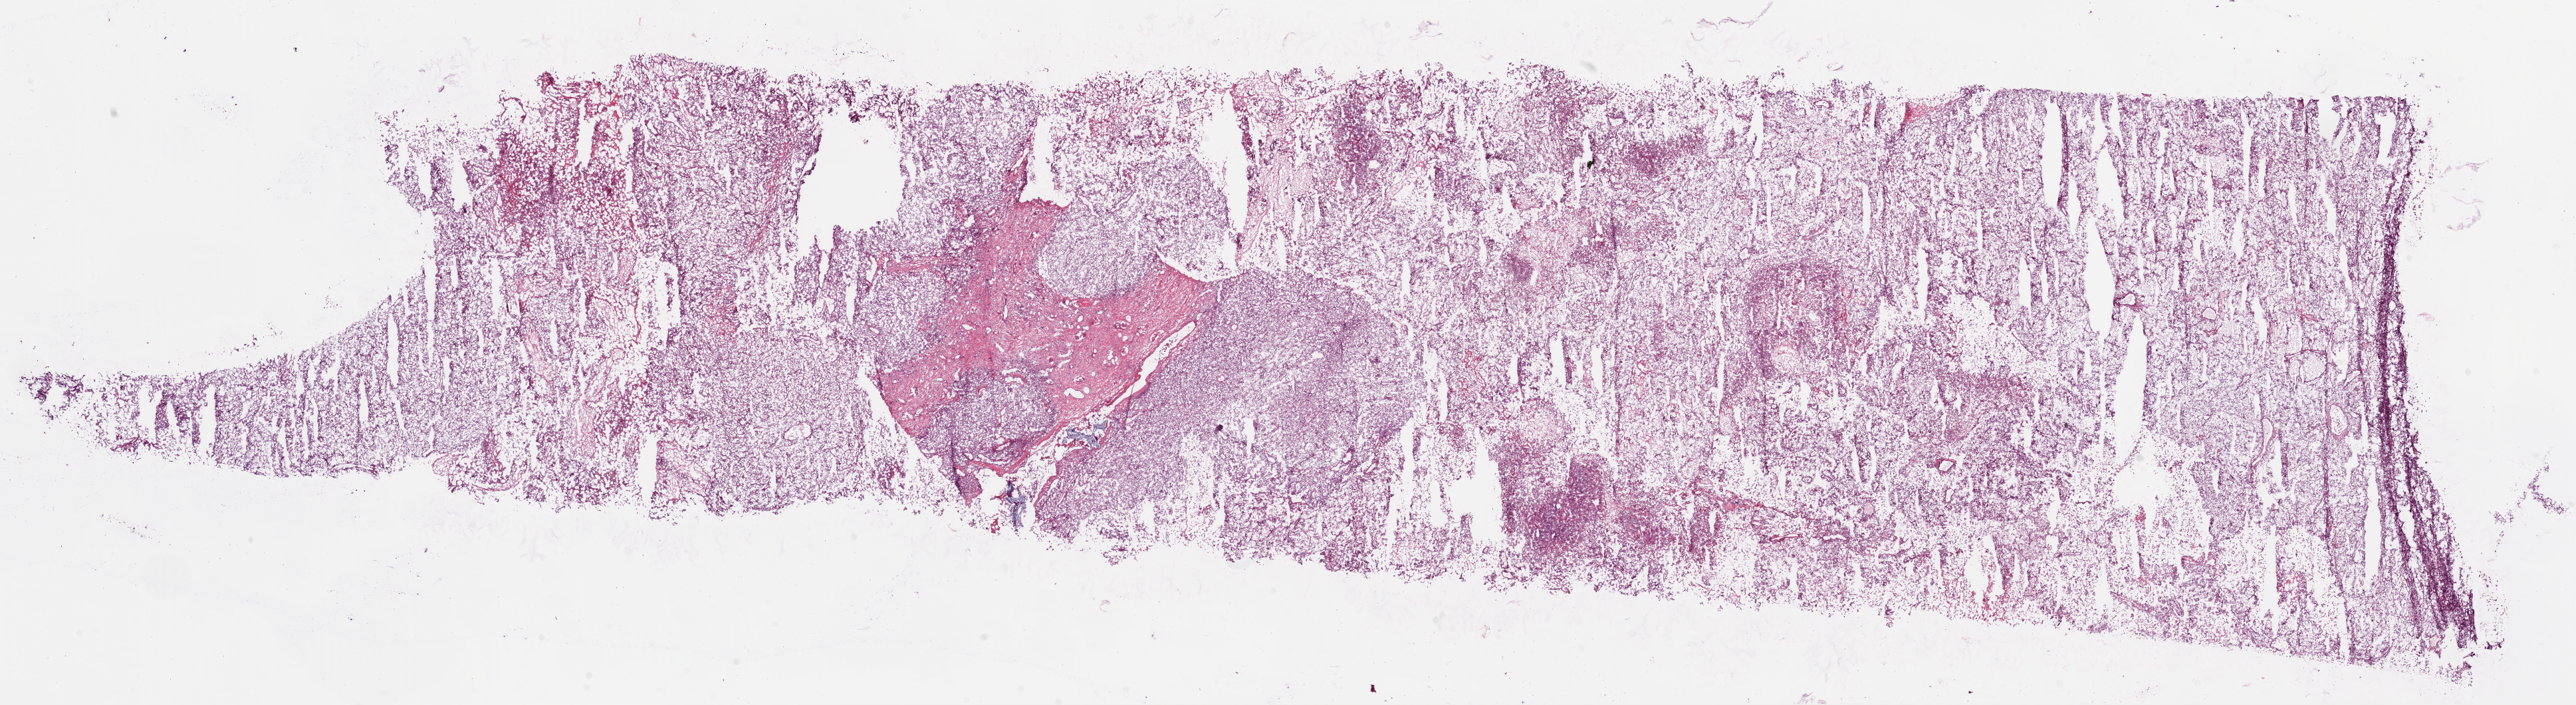
Whole-slide histology image, Hematoxylin and eosin (H&E) stained — a low-resolution overview of the entire scanned area, about 31.1 x 8.5 mm (from a 20x scan); frozen section from the bottom of the tissue portion; primary tumour sample from the kidney. Patient: female, age at initial diagnosis 57 years. Histologic grade: G4 (undifferentiated). Pathologist review of this section (percent, as recorded): tumour cells 75%, tumour nuclei 80%, normal cells 0%, stromal cells 15%, necrosis 10%.
- pathologic diagnosis: Clear cell adenocarcinoma, NOS
- AJCC pathologic stage: III (7th edition)
- laterality: left